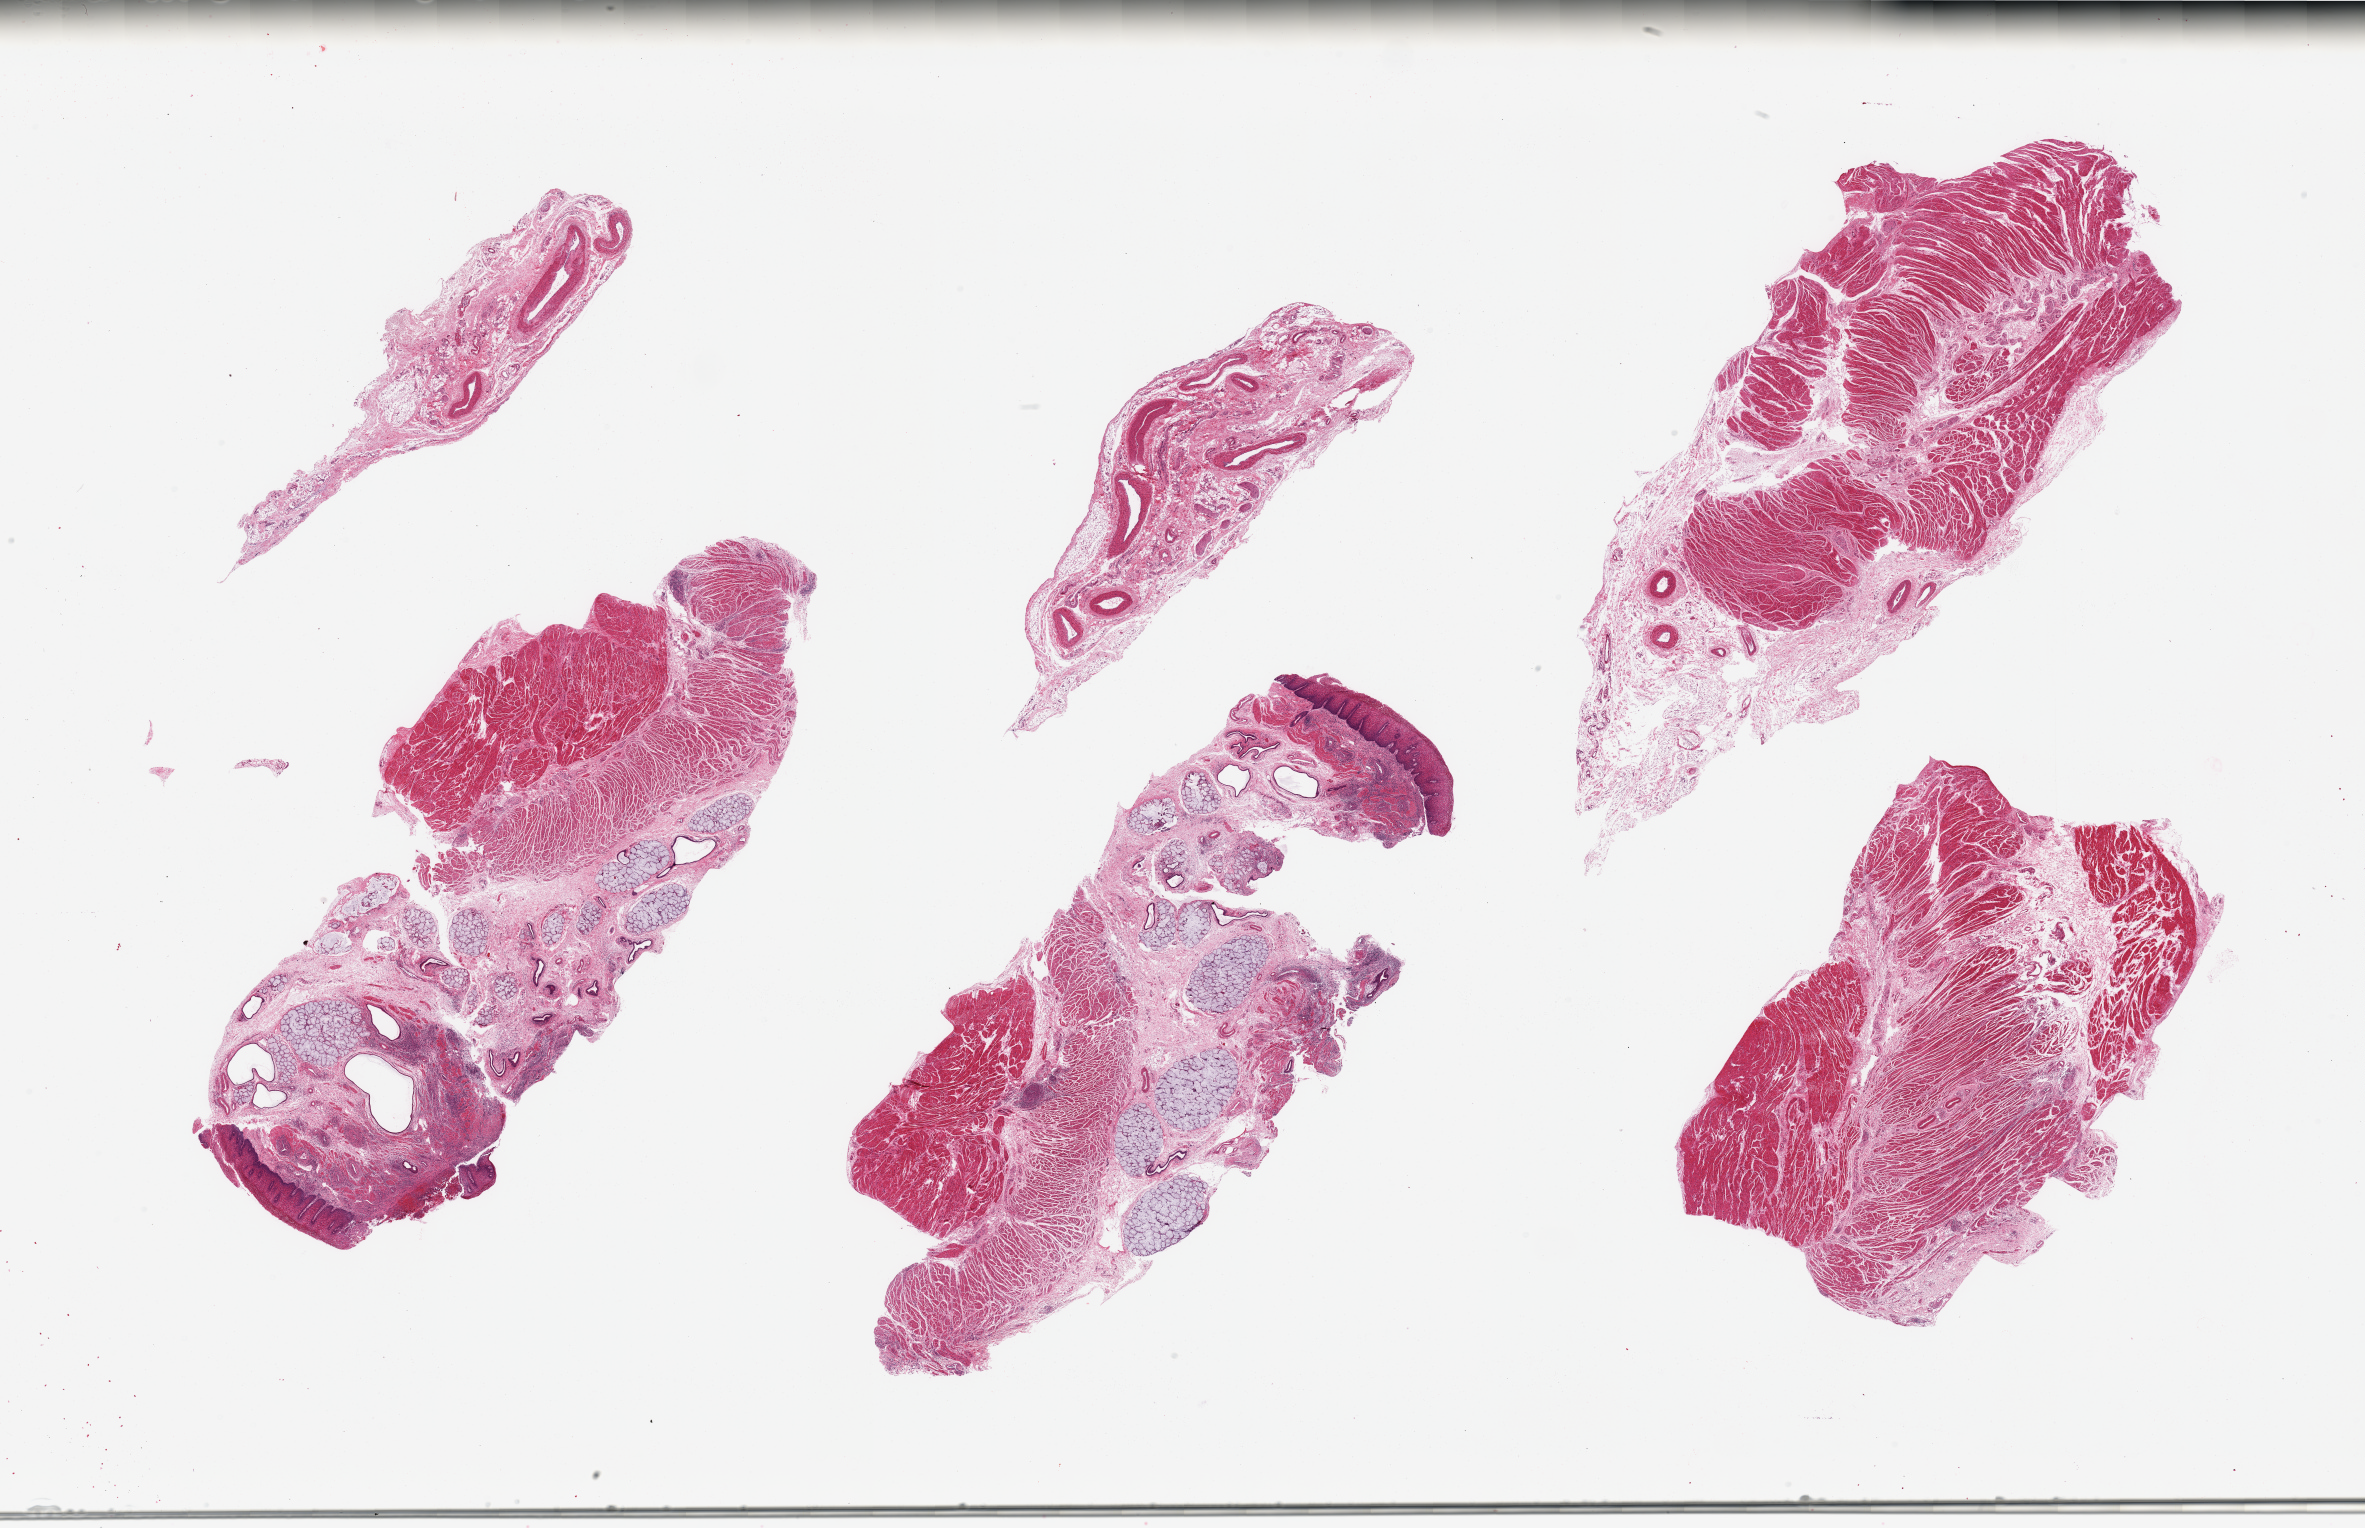
Haematoxylin and eosin whole-slide image — a low-resolution overview of the entire scanned area, about 37.4 x 24.2 mm. PAXgene-fixed, paraffin-embedded tissue. Section of gastroesophageal junction (target tissue). Tissue donor sample. Donor: female.
* pathologist's review note for this sample: 6 pieces, <50% target muscularis: stroma, squamous mucosa, mucus gland are >50% of specimen